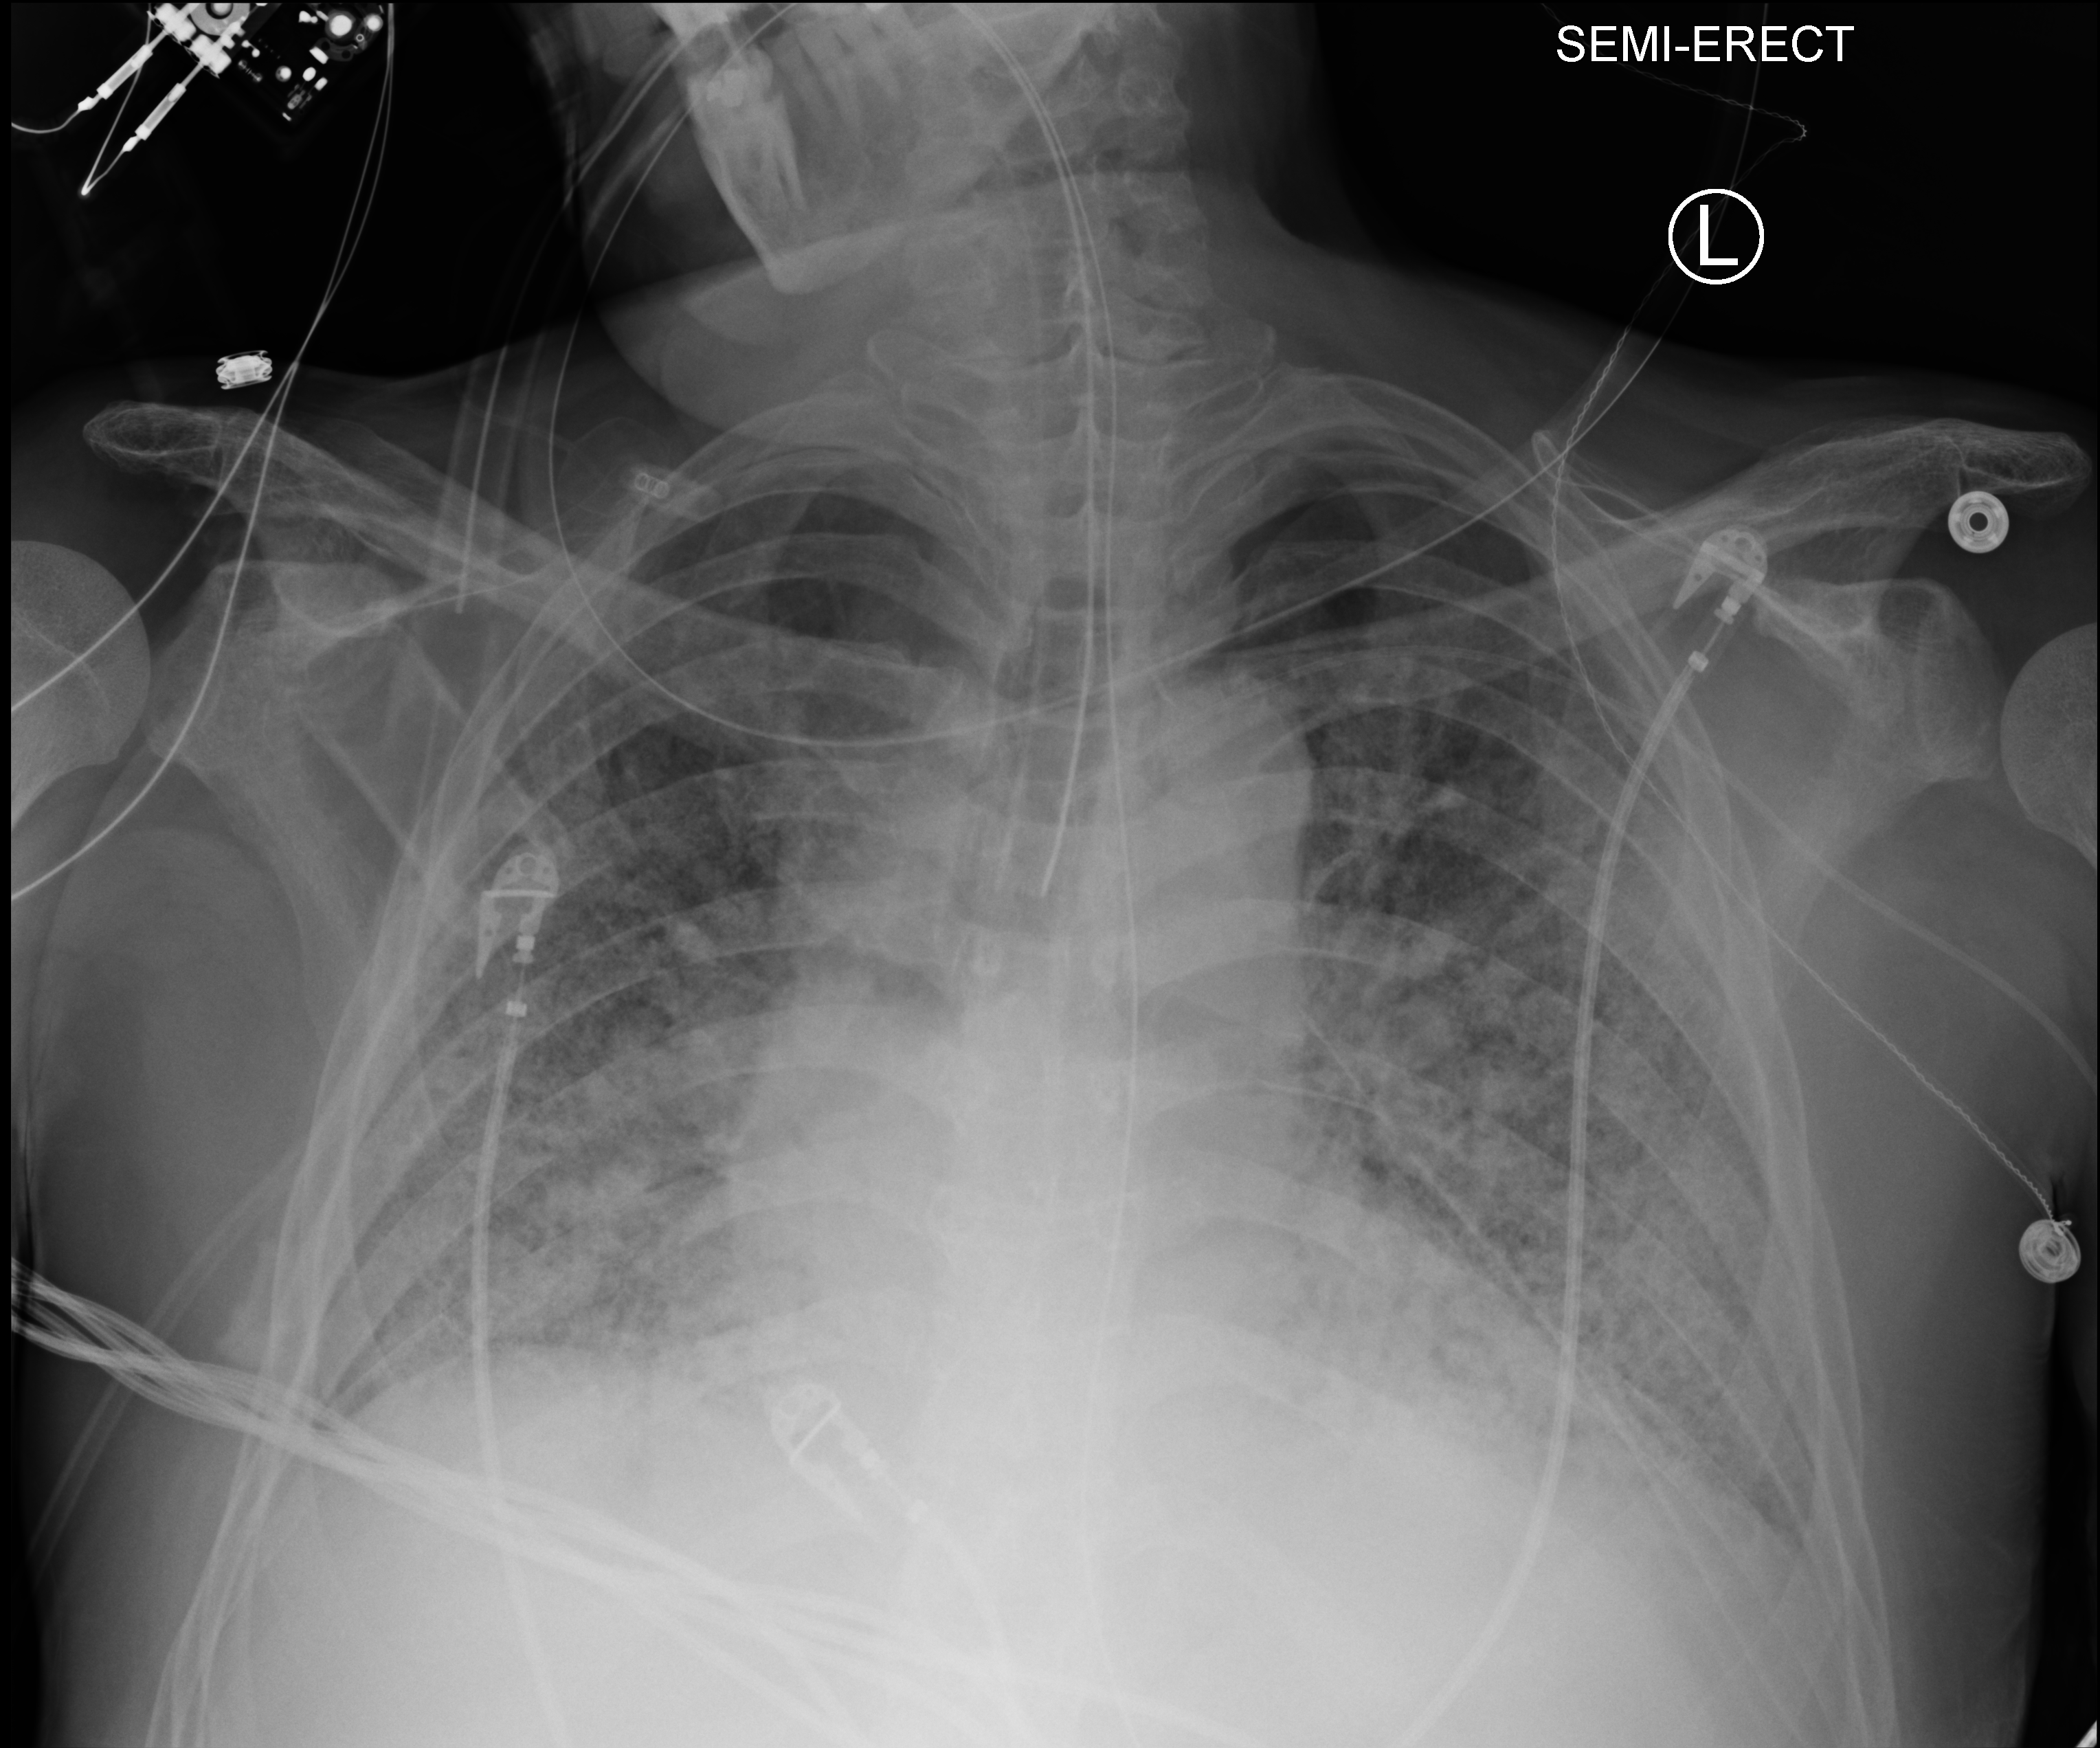
Portable chest radiograph, anteroposterior (AP) projection. Male patient hospitalised with COVID-19, age 60–74 years.
From the hospital-stay record, not from the radiograph (when in the stay this image was taken is not recorded): mechanically ventilated during this hospital stay: yes.